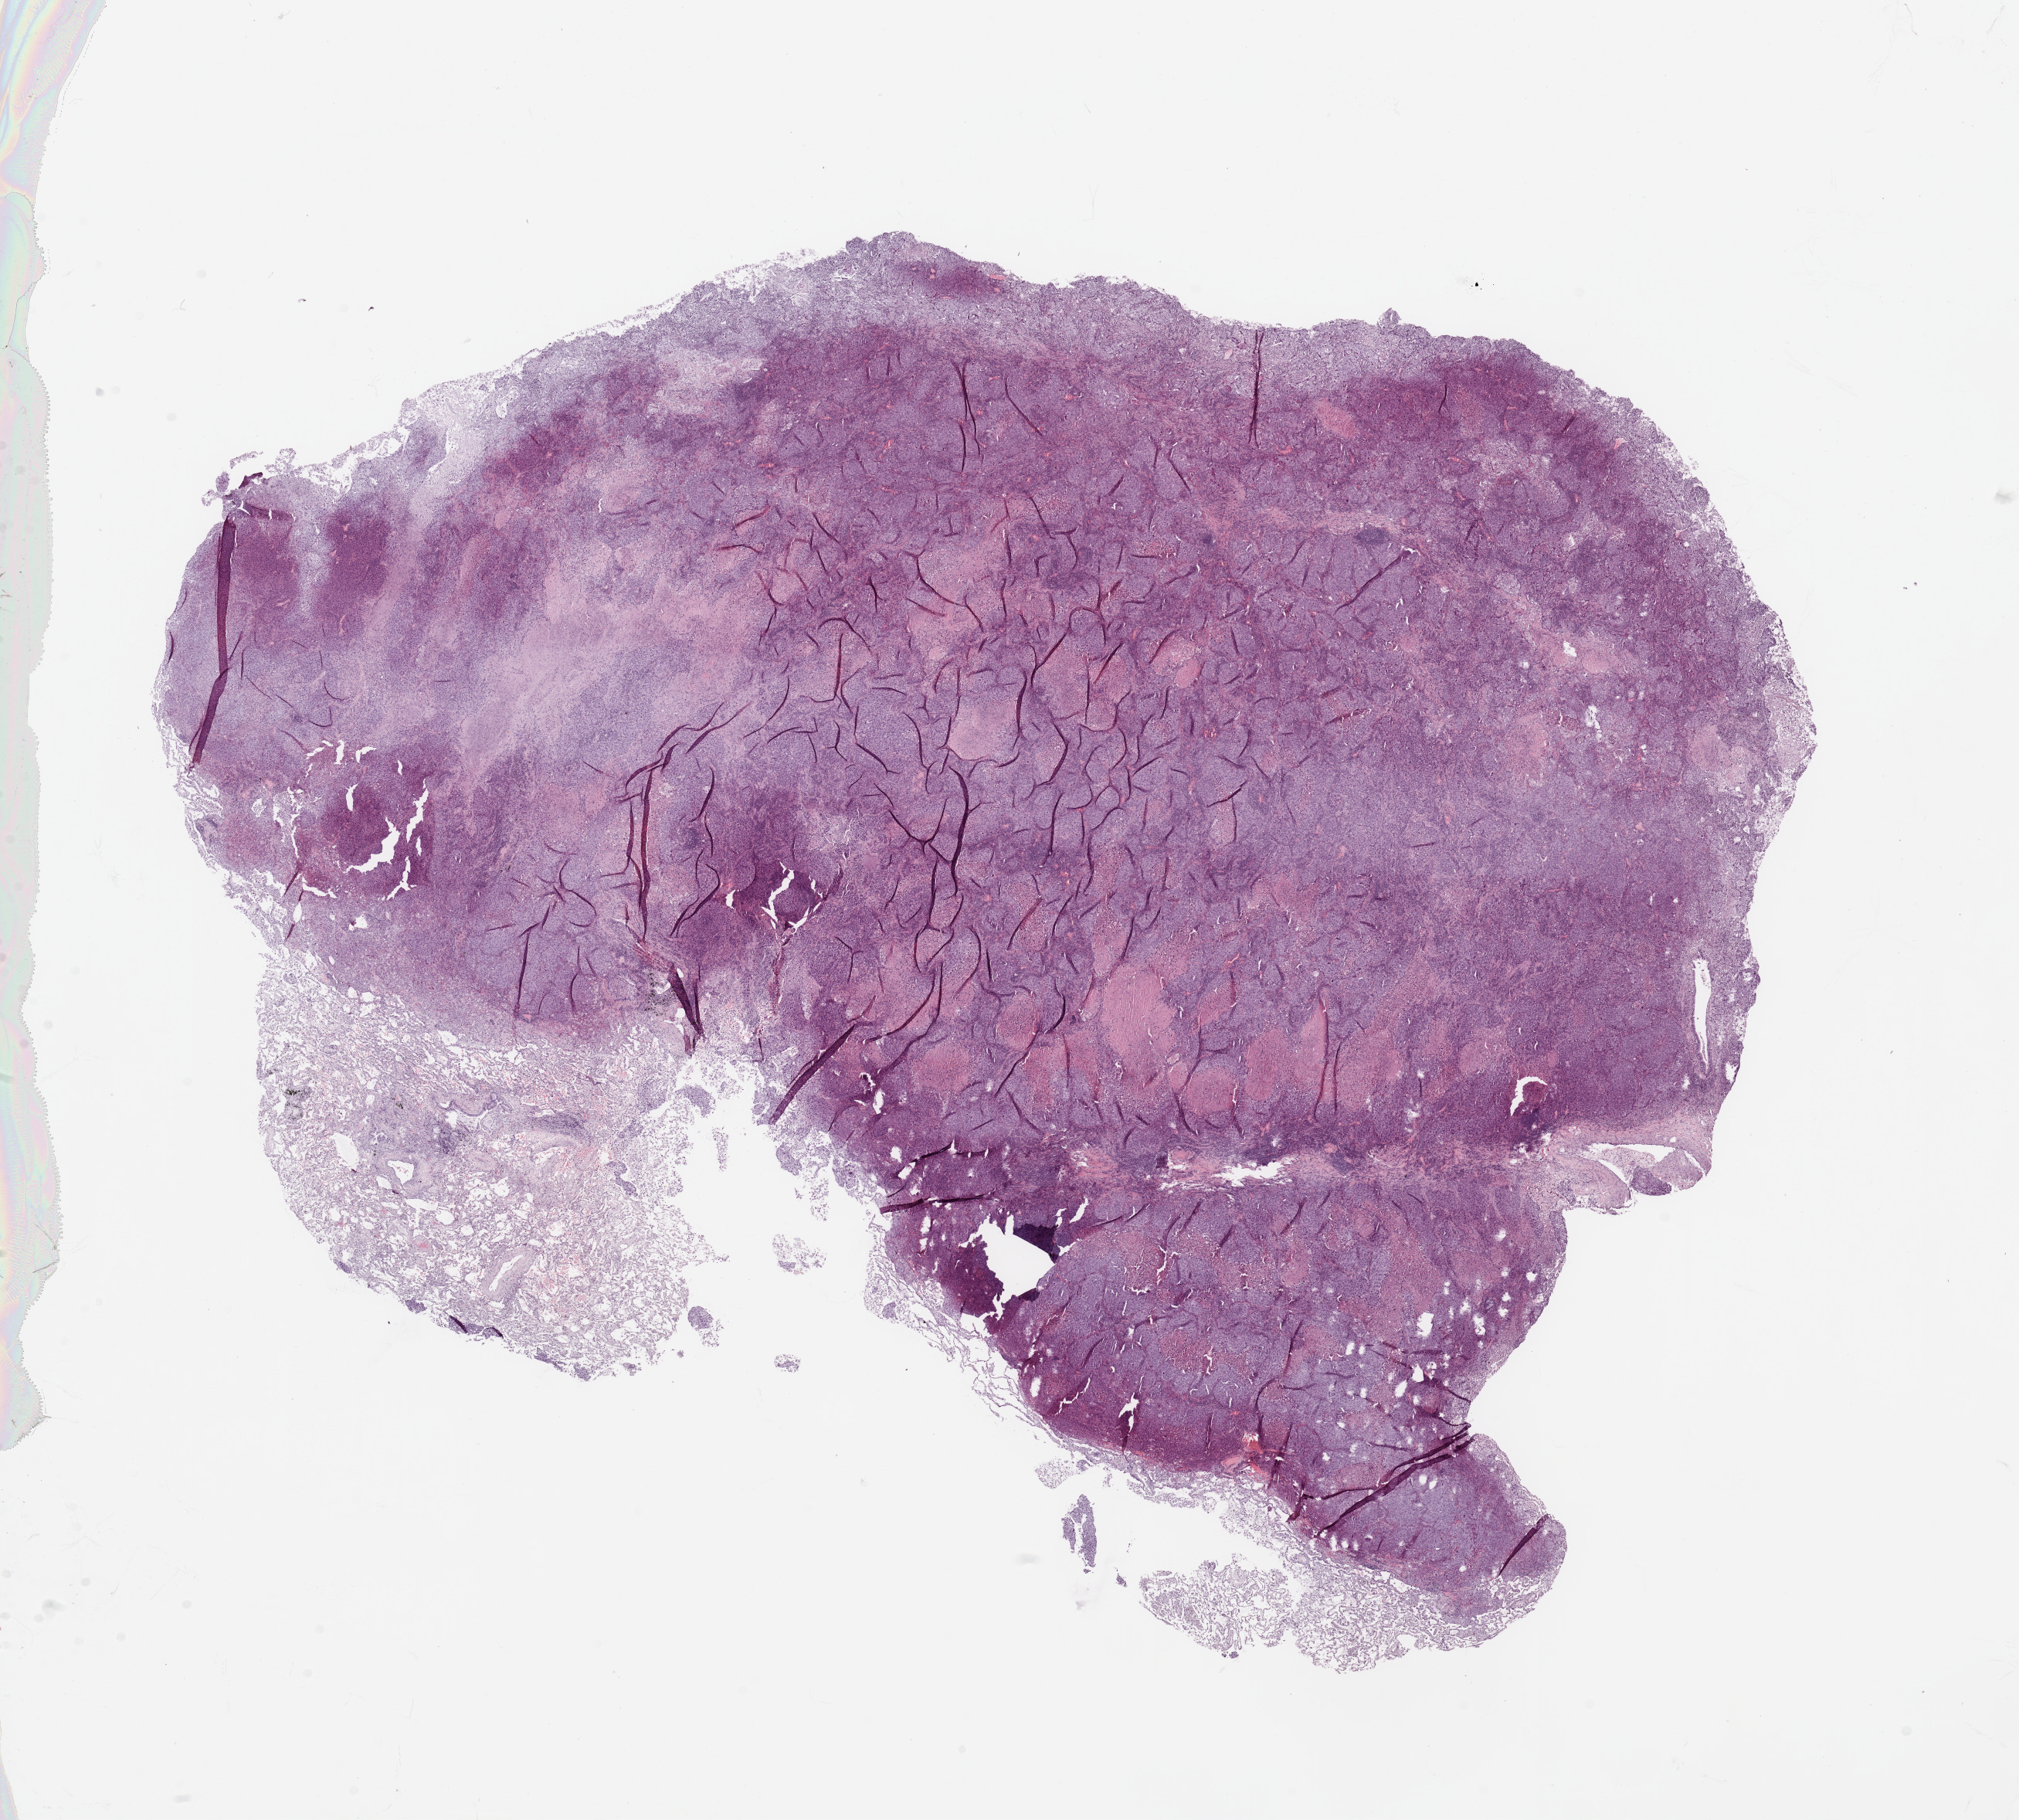
Digitized H&E-stained tissue section (whole slide), a low-resolution overview of the entire scanned area, about 20.7 x 18.6 mm. Lung, tumour tissue. Male, 61 y/o. Histologic grade: G2 (moderately differentiated).
* primary tumour site (as recorded): right upper lobe
* diagnosis: Squamous cell carcinoma, NOS